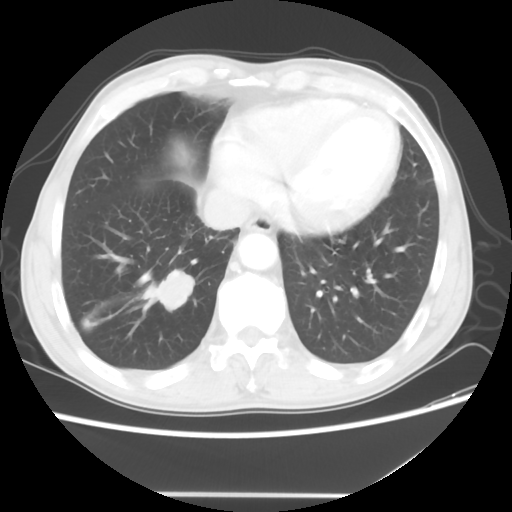
Chest CT, one axial slice. Slice 13 of 56 in the series (ordered by position). Reconstruction kernel STANDARD. 120 kVp. Lung window (W 1500 / L -600 HU). 5 mm slice thickness. 512 × 512 image matrix. Patient: male, 65 years. From the clinical record (not read from this slice): clinical TNM (as recorded): T1c N3 M0; histopathological grade: G3.
Outlined on this slice (bounding box drawn by a radiologist):
- lung tumour (recorded histology: small cell carcinoma): bounding box (x1, y1, x2, y2) in pixels: (140, 263, 195, 317)